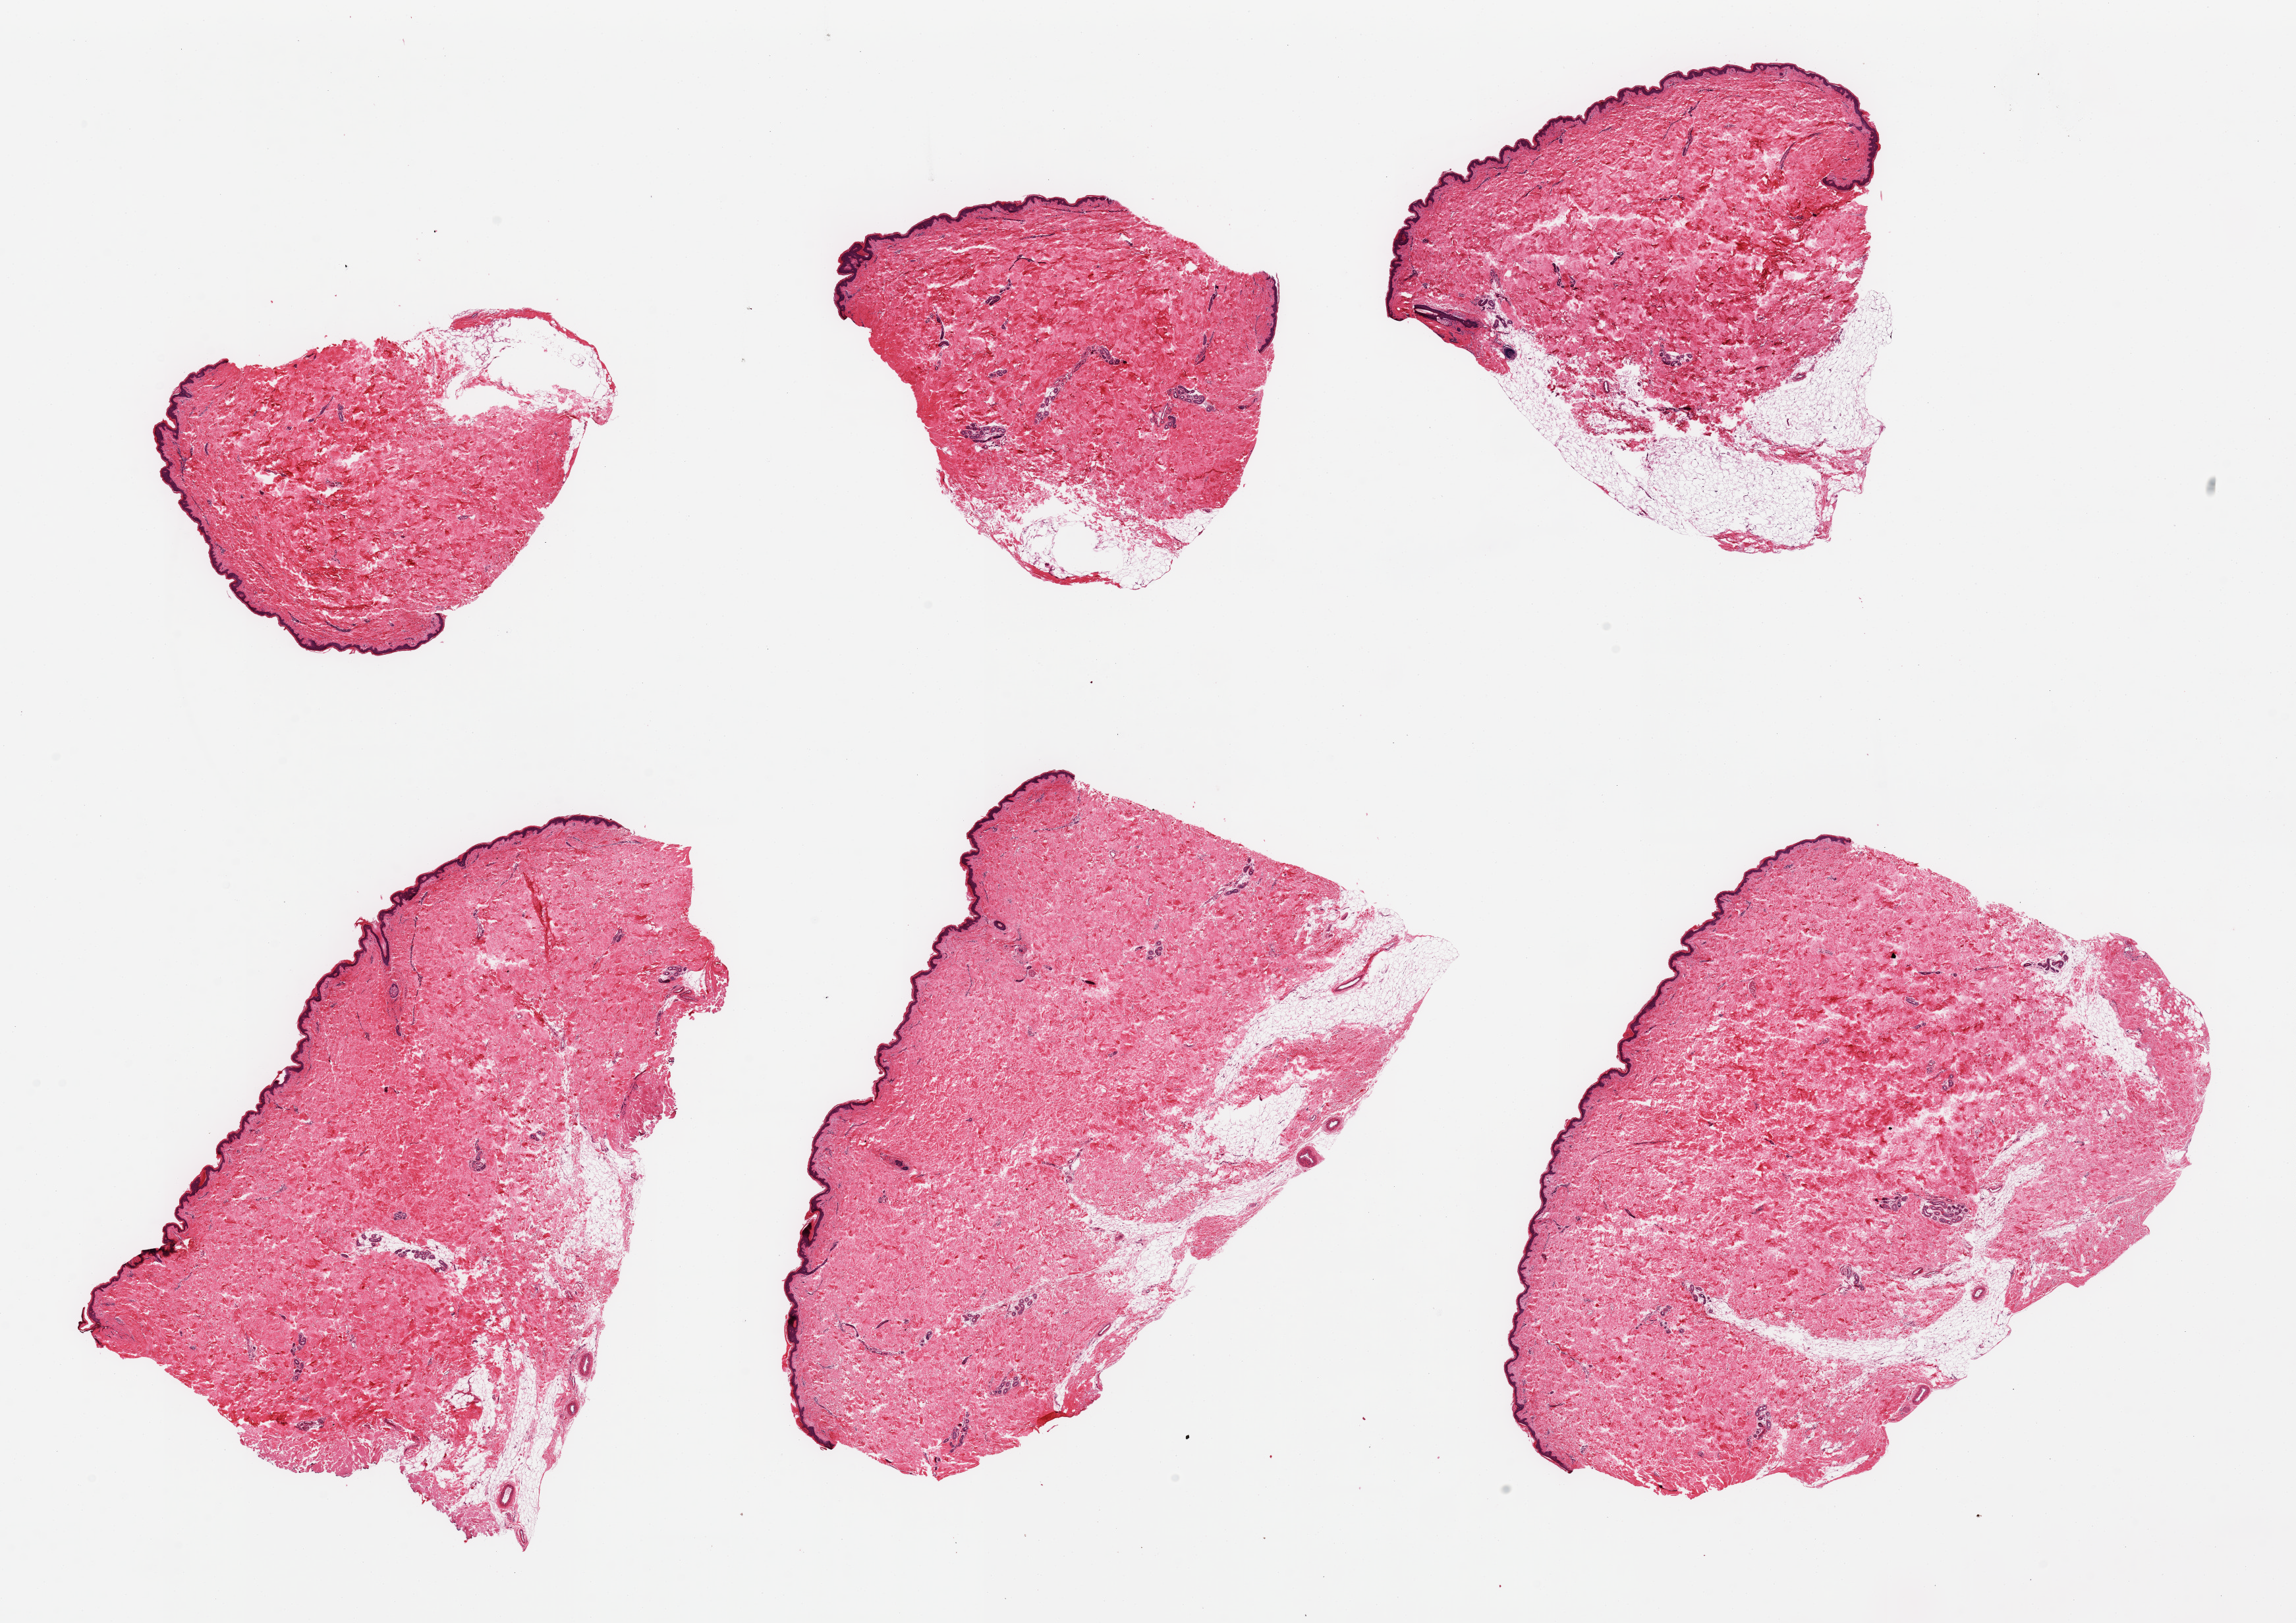
Digitized haematoxylin and eosin-stained section — whole scanned area (about 27.6 x 19.5 mm) shown as a low-resolution overview; PAXgene-fixed paraffin-embedded (PFPE) section; sampled site (target tissue): skin of suprapubic region; tissue donor sample. Female donor.
Pathologist's review note for this sample: 6 pieces, squamous epithelium is ~35-40 microns; adherent nubbins dermal fat up to ~1.5mm.